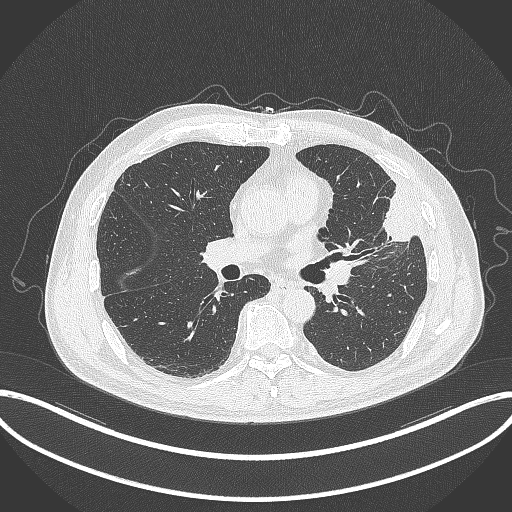
Chest CT, one axial slice. Position 178 of 382 along the scan axis. 120 kVp. Lung window (W 1500 / L -600 HU). 1 mm slice thickness. 512 × 512 image matrix, field of view 415 × 415 mm. Male patient, age 64 years. From the clinical record (not read from this slice): clinical TNM (as recorded): T4 N1 M0.
Outlined on this slice (rectangle marked by the reading radiologist):
- lung tumour (recorded histology: adenocarcinoma): bounding box (x1, y1, x2, y2) in pixels: (370, 186, 427, 253)